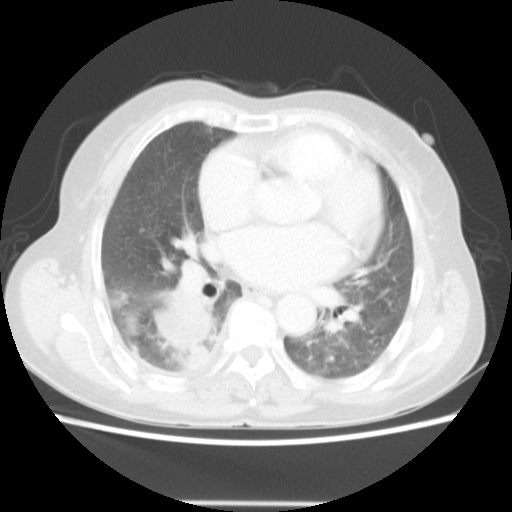
Chest CT, one axial slice. Position 25 of 52 along the scan axis. Reconstruction kernel STANDARD. Lung window (W 1500 / L -600 HU). 5 mm slice thickness. 512 × 512 image matrix. Patient: female, 67 years. Case-level facts recorded for this patient, not image findings: clinical TNM (as recorded): T3 N1 M1.
Outlined on this slice (rectangle marked by the reading radiologist):
- lung tumour (recorded histology: adenocarcinoma): box from (x=148, y=285) to (x=219, y=368) px